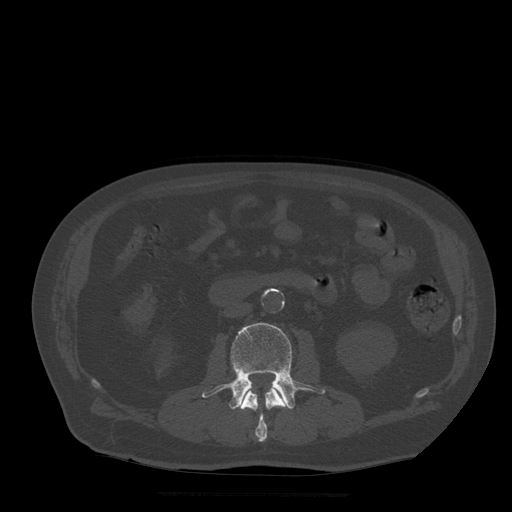
CT including the spine, one axial slice; slice 151 of 522 in the series (ordered by position); bone window (W 1800 / L 400 HU); 1.25 mm slice thickness; 512 × 512 image matrix, field of view 420 × 420 mm. Patient age 72 years. Case-level facts recorded for this patient, not image findings: primary cancer: prostate.
Outlined on this slice (semi-automatically segmented with operator editing):
- L2 vertebra: bounding box (x1, y1, x2, y2) in pixels: (241, 386, 287, 442)
- L3 vertebra: (202, 323, 325, 410)